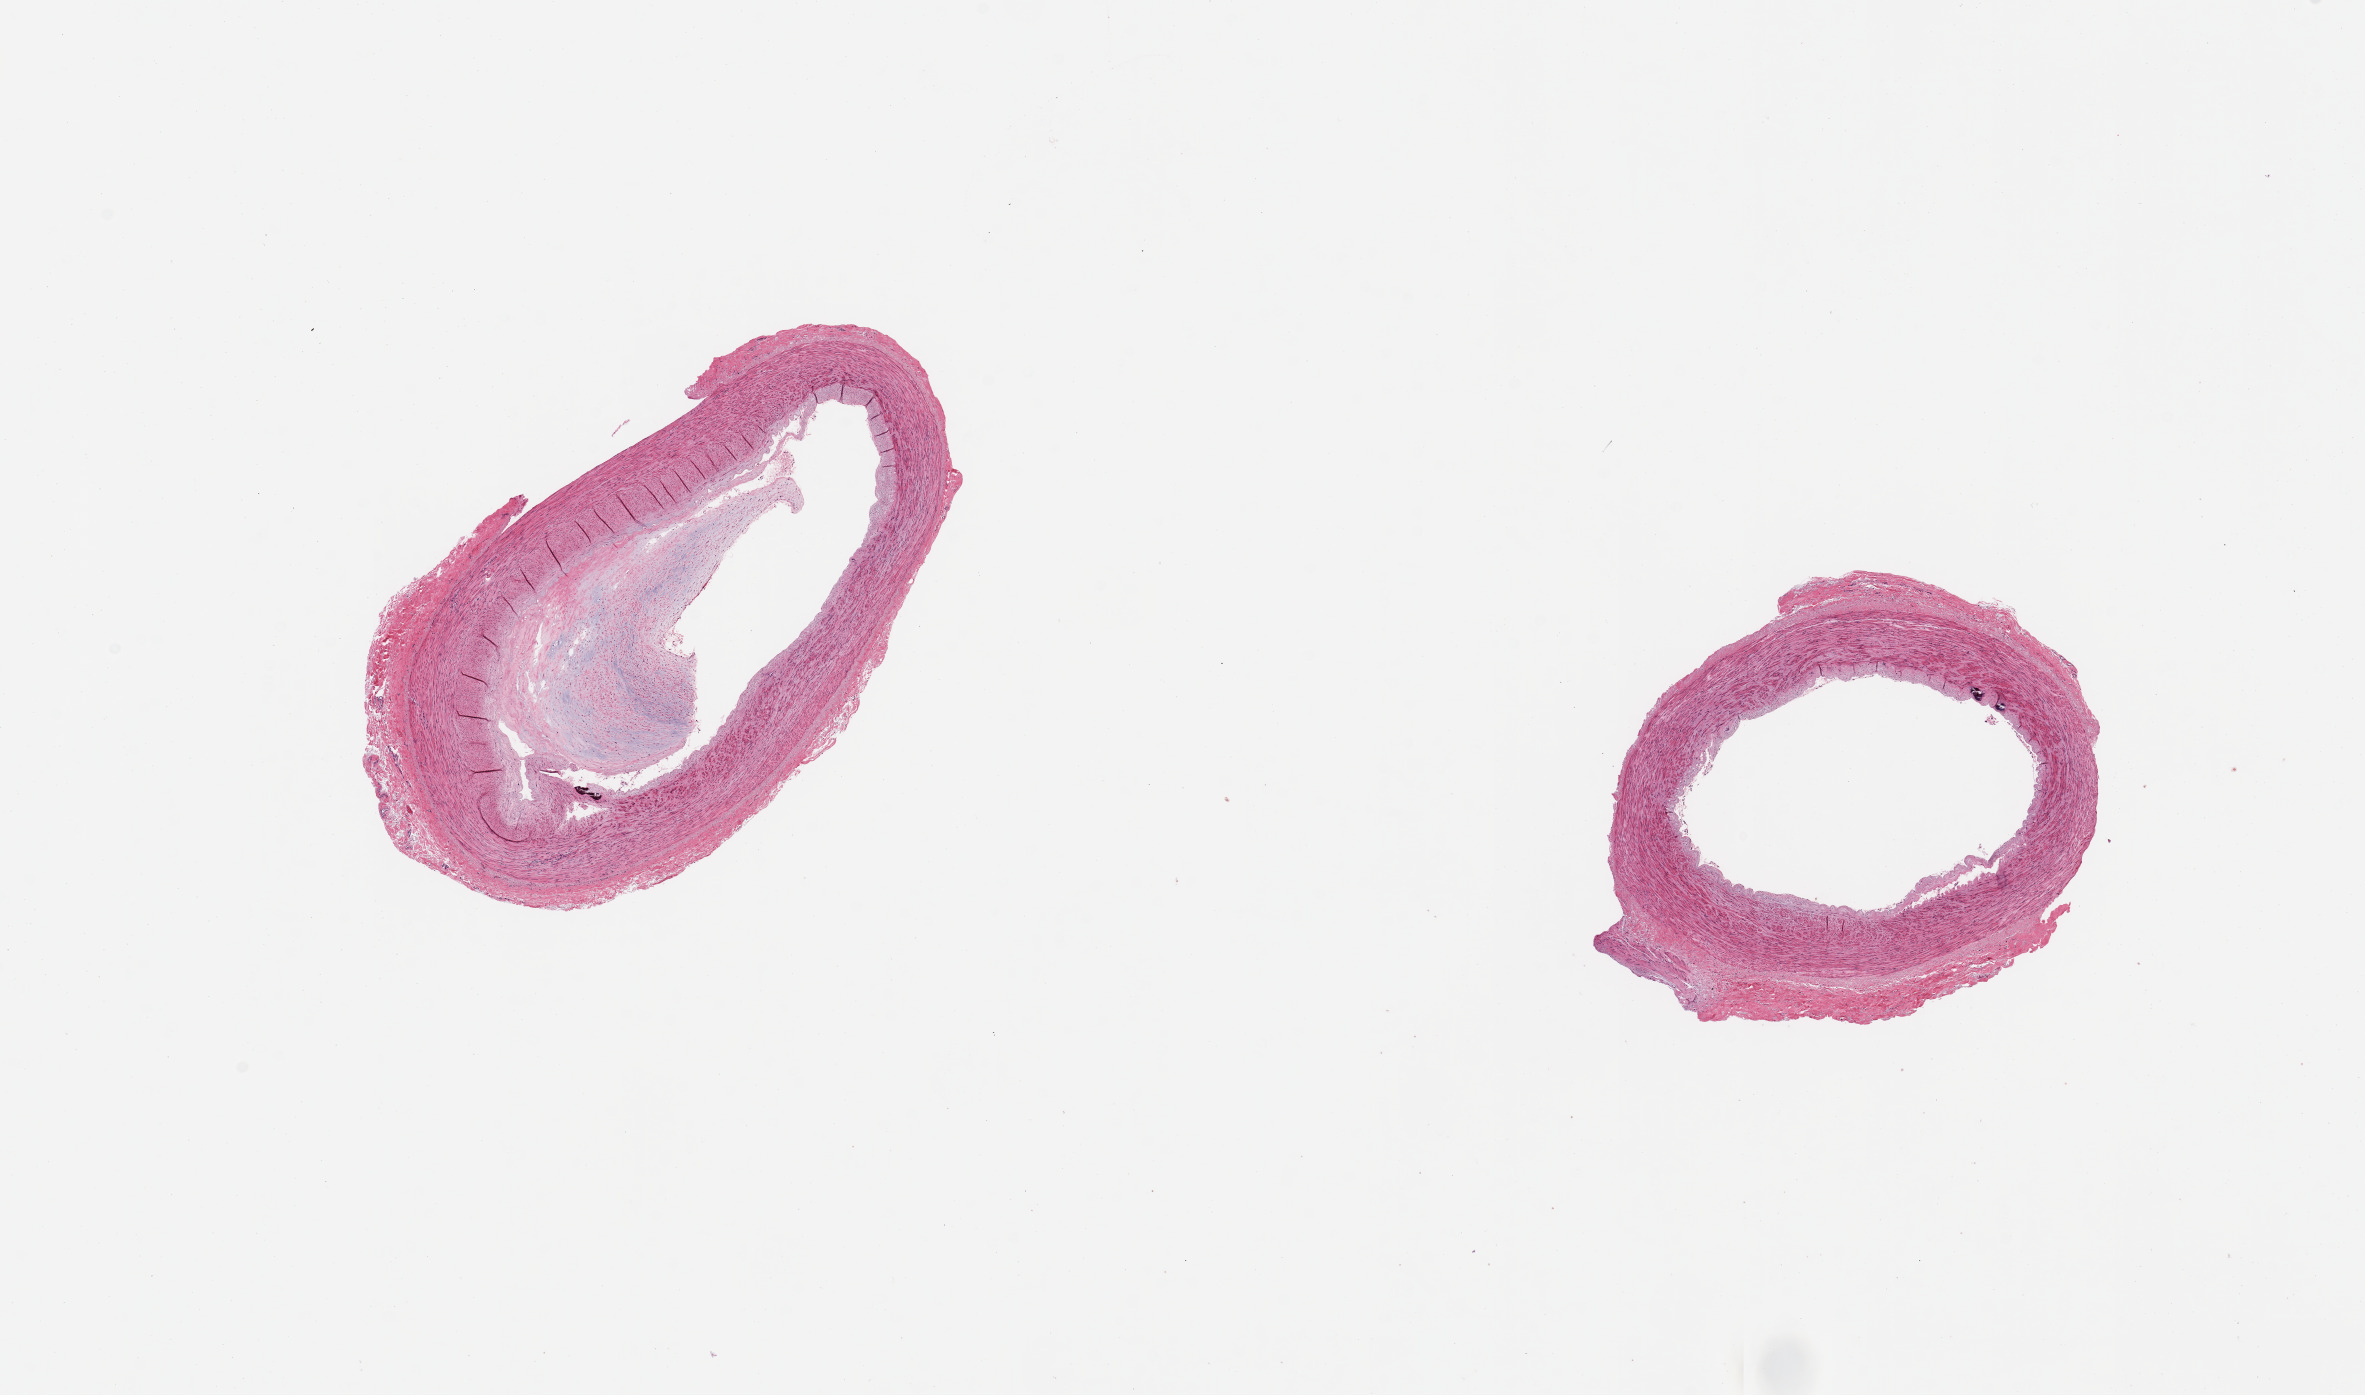
Hematoxylin and eosin (H&E) whole-slide image, whole scanned area (about 18.7 x 11.0 mm, from a 20x scan) shown as a low-resolution overview, PAXgene-fixed, paraffin-embedded tissue, sampled site (target tissue): tibial artery, tissue donor sample. Donor: male.
Review note (as recorded): 2 pieces; 1 with large eccentric fibrotic intimal plaque; small calcific intimal deposits in both pieces.